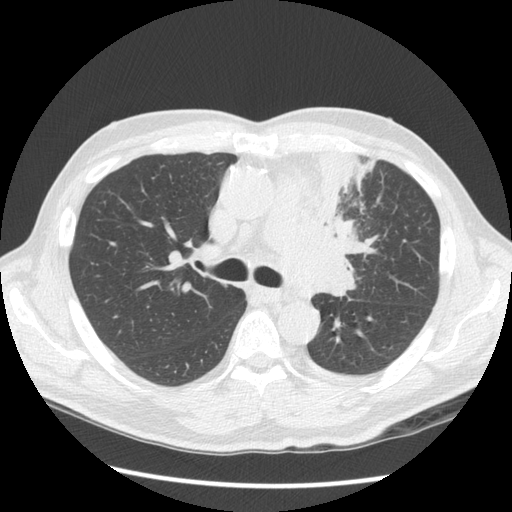
Low-dose screening chest CT, one axial slice. Slice 90 of 136 in the series (ordered by position). Lung window (W 1500 / L -600 HU). 2.5 mm slice thickness. 512 × 512 image matrix.
Annotated regions visible in this slice (outlined manually by an expert reader):
- lesion 1 (tumor, upper lobe of left lung): box from (x=284, y=147) to (x=374, y=298) px